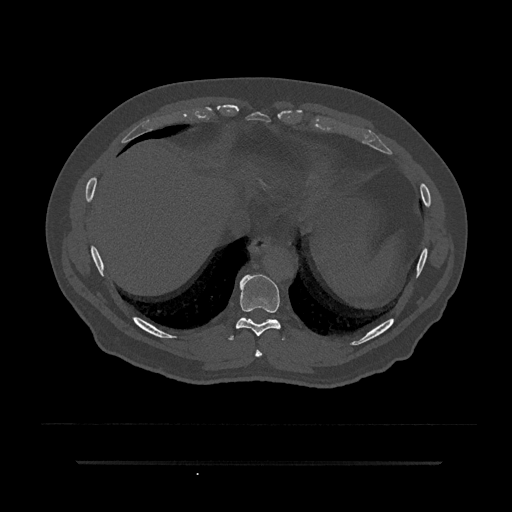
CT including the spine, one axial slice. 120 kVp. Bone window (W 1800 / L 400 HU). 0.5 mm slice thickness. 512 × 512 image matrix, field of view 464 × 464 mm. Patient: male, 59 years. From the clinical record (not read from this slice): primary cancer: bile ducts.
Annotated regions visible in this slice (semi-automatically segmented with operator editing):
- T8 vertebra: bounding box [x1, y1, x2, y2] px = [255, 349, 262, 357]
- T9 vertebra: [228, 274, 285, 341]